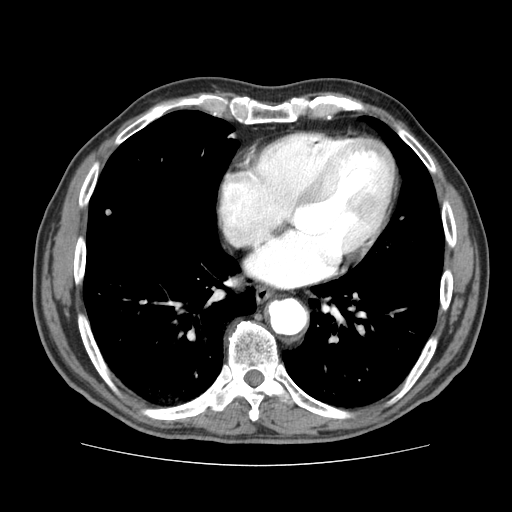
Contrast-enhanced abdominal CT (liver protocol), one axial slice; slice 78 of 79 in the series (ordered by position); 120 kVp; soft-tissue window (W 400 / L 40 HU); 2.5 mm slice thickness; 512 × 512 image matrix. Case-level facts recorded for this patient, not image findings: diagnosis: hepatocellular carcinoma (patient treated with transarterial chemoembolisation; whether this scan precedes or follows treatment is not stated here); TNM stage (as recorded): Stage-I; Child-Pugh class: A; tumour nodularity: uninodular.
Structures marked on this image (semi-automatic segmentation, software-assisted and operator-edited):
- abdominal aorta: box from (x=269, y=299) to (x=306, y=334) px